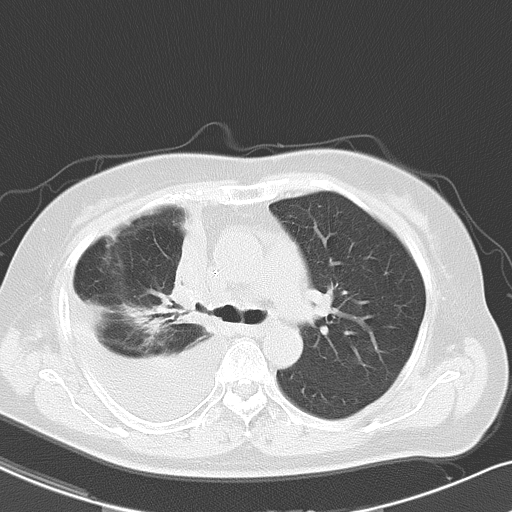
Chest CT, one axial slice. Slice 33 of 48 in the series (ordered by position). Reconstruction kernel B70f. Lung window (W 1500 / L -600 HU). 5 mm slice thickness. 512 × 512 image matrix, field of view 328 × 328 mm. Patient: female, 69 years. Case-level facts recorded for this patient, not image findings: clinical TNM (as recorded): T2a N0 M1c.
Outlined on this slice (bounding box drawn by a radiologist):
- lung tumour (recorded histology: adenocarcinoma): bounding box (x1, y1, x2, y2) in pixels: (162, 206, 213, 330)